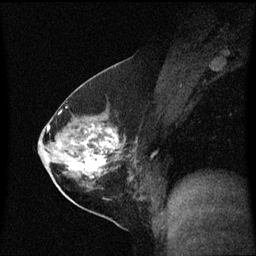
Breast MRI (dynamic contrast-enhanced), one sagittal slice; slice 31 of 60 in the series (ordered by position); dynamic contrast-enhanced series, image 2 of 3 at this slice position (ordered by acquisition); 1.5 T; TE 4.2 ms, TR 8.4 ms; 2 mm slice thickness; 256 × 256 image matrix. Patient: female, 54 years. Case-level facts recorded for this patient, not image findings: setting: breast cancer imaged before/during neoadjuvant chemotherapy; receptor status: HER2-positive.
Structures marked on this image (semi-automatically segmented with operator editing):
- analysis volume of interest (the breast-tissue region the enhancement analysis was run in; not a lesion): bounding box <59,115,141,199> (left, top, right, bottom; pixels)
- tumour enhancement mask (voxels above the 70 % enhancement threshold inside the analysis volume of interest): <69,126,120,174>